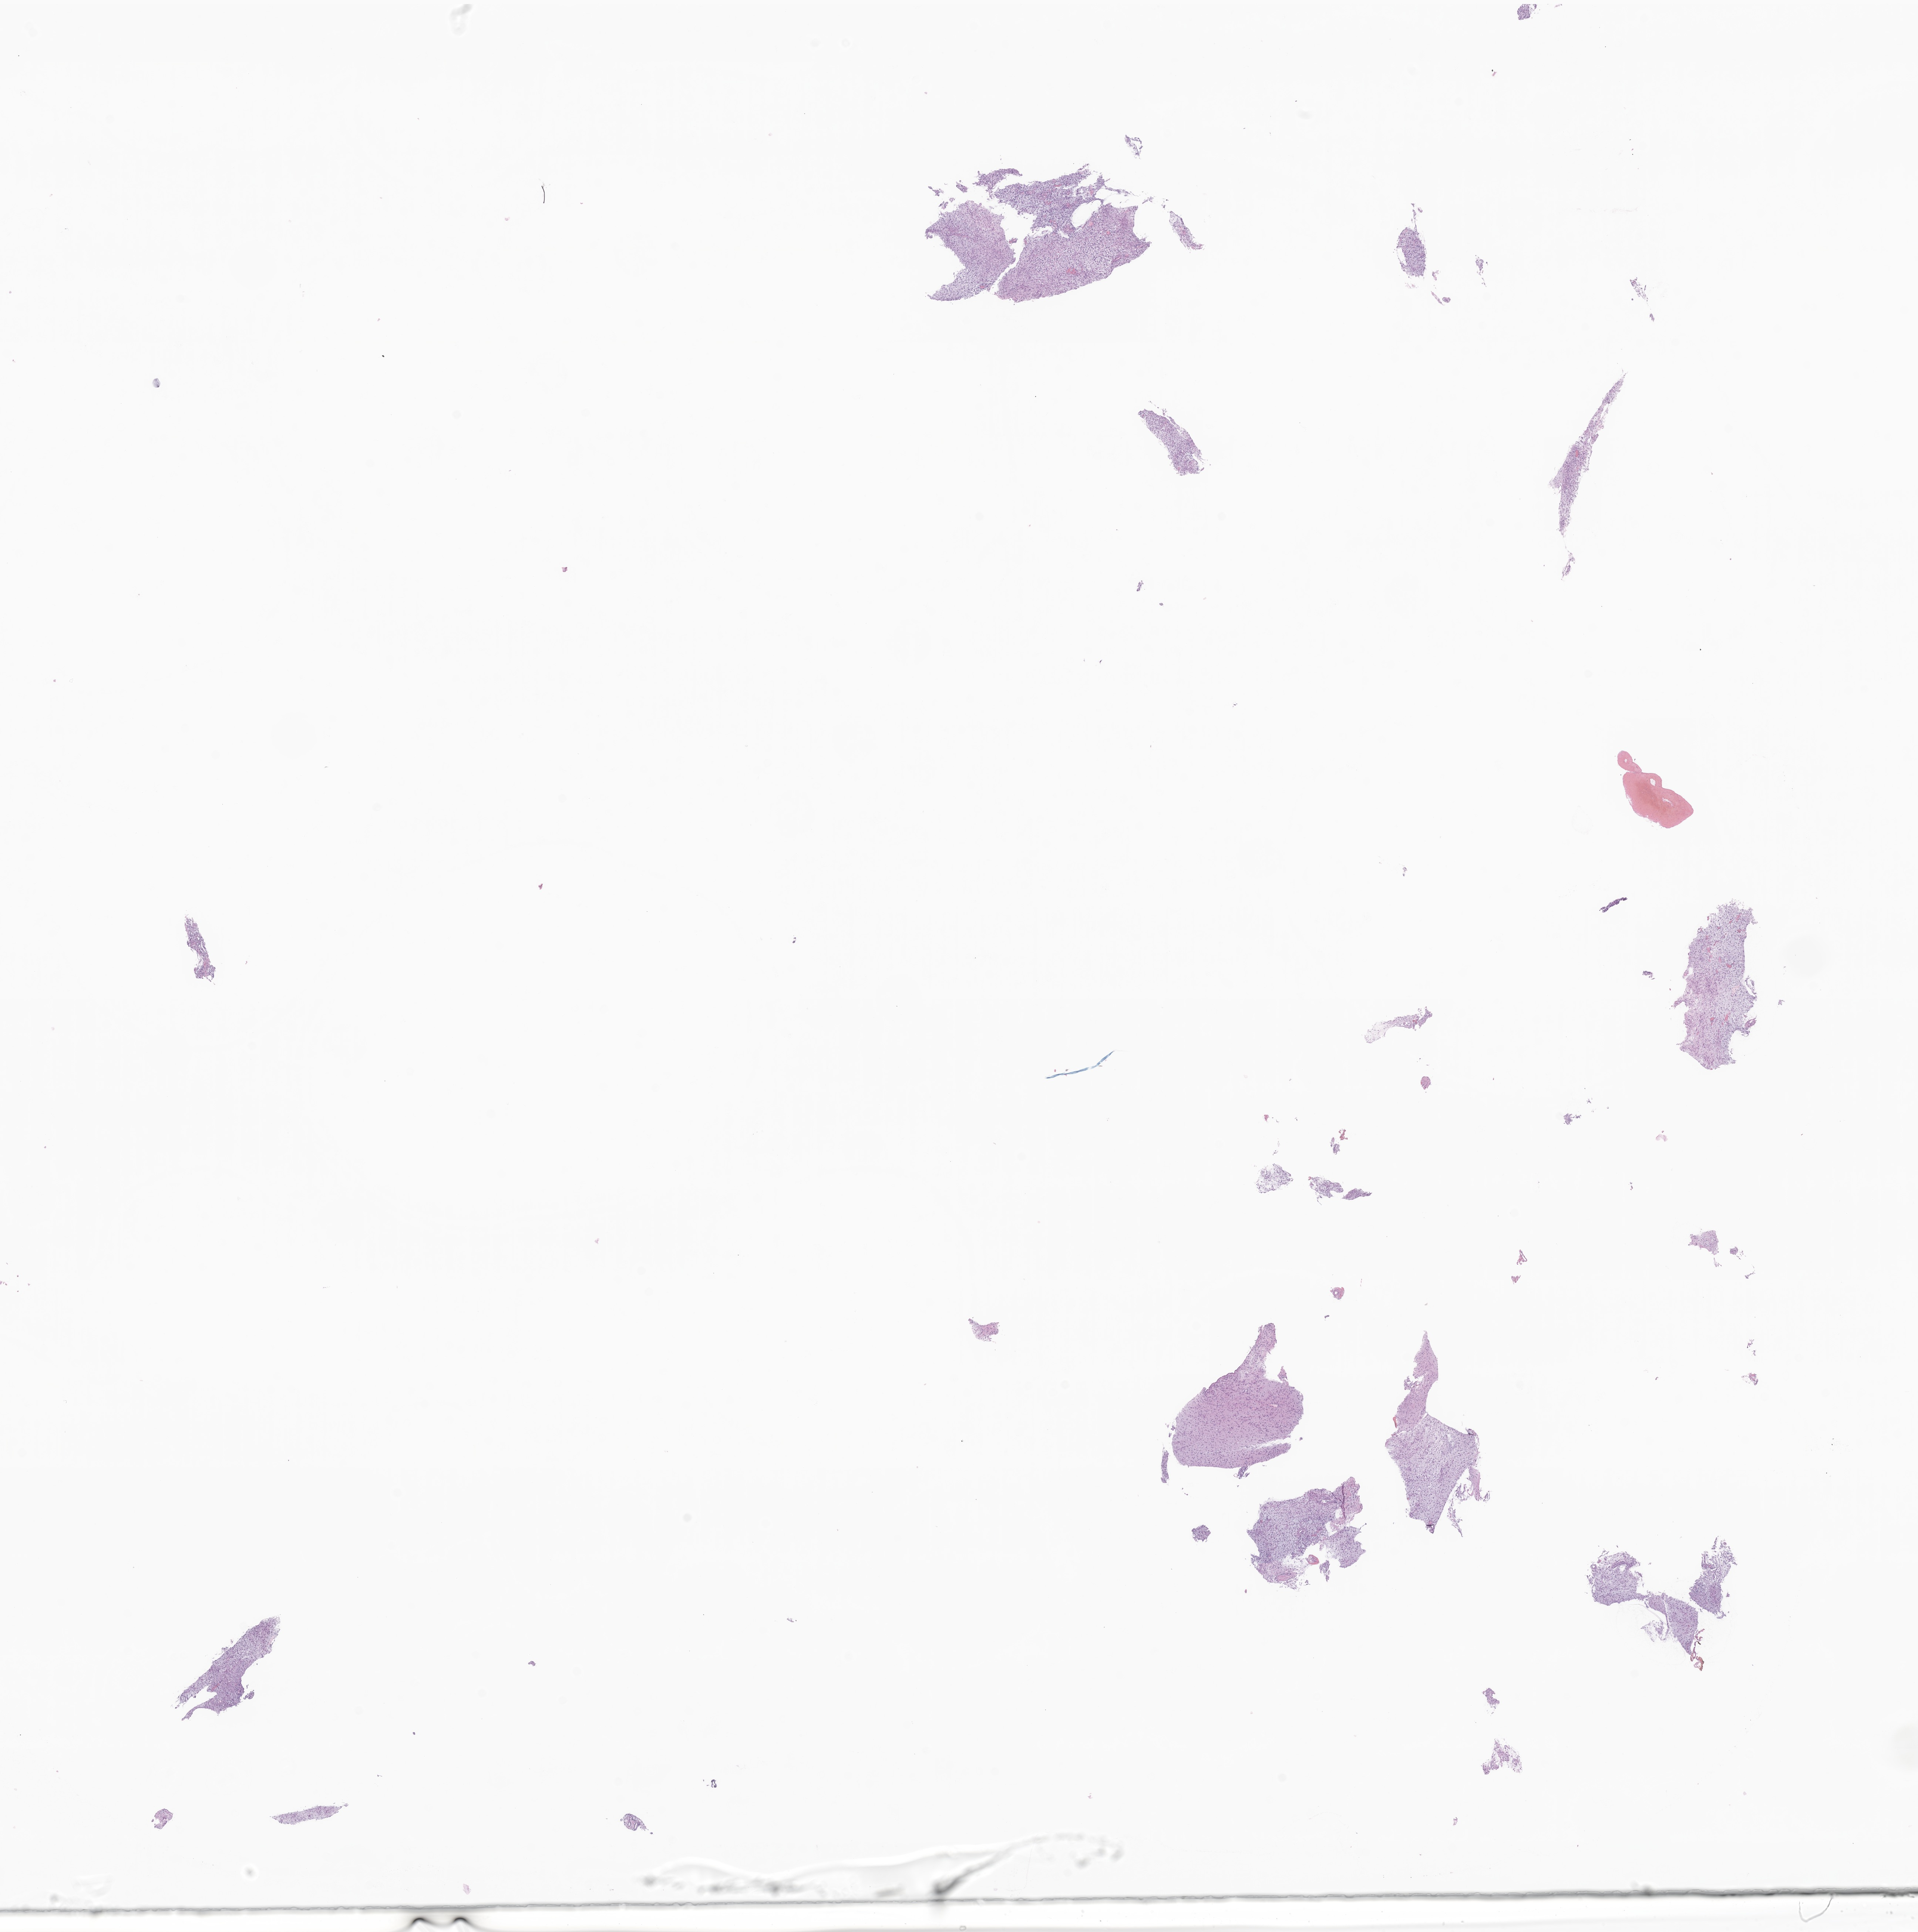
Digitized hematoxylin and eosin (H&E)-stained section of tumor tissue from the cerebral ventricle — a low-resolution overview of the entire scanned area, about 21.9 x 22.0 mm. Formalin-fixed, paraffin-embedded (FFPE) tissue. Male patient, age 144 months (12 years).
• recorded diagnosis: Pilocytic astrocytoma